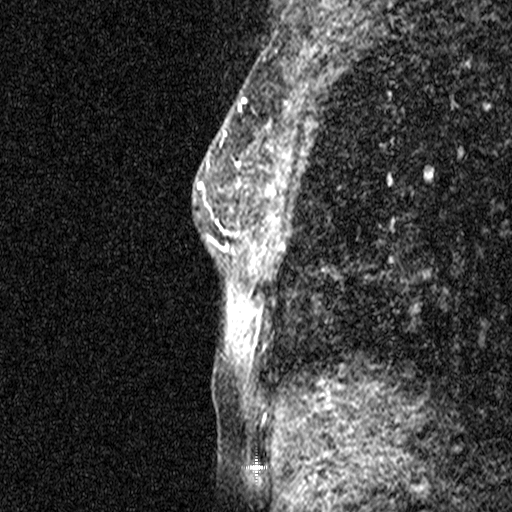
Breast MRI (dynamic contrast-enhanced), one sagittal slice. Position 22 of 44 along the scan axis. Dynamic contrast-enhanced study with each time point stored as its own series, time point 2 of 3 at this slice position (early post-contrast, ordered by acquisition time). 1.5 T. TE 4.5 ms, TR 11 ms. 512 × 512 image matrix. Female patient, age 44 years. Case-level facts recorded for this patient, not image findings: setting: breast cancer imaged before/during neoadjuvant chemotherapy; receptor status: HR-positive, HER2-negative.
Structures marked on this image (semi-automatically segmented with operator editing):
- analysis volume of interest (the breast-tissue region the enhancement analysis was run in; not a lesion): bounding box [x1, y1, x2, y2] px = [218, 118, 271, 291]
- tumour enhancement mask (voxels above the 90 % enhancement threshold inside the analysis volume of interest): [218, 132, 240, 222]